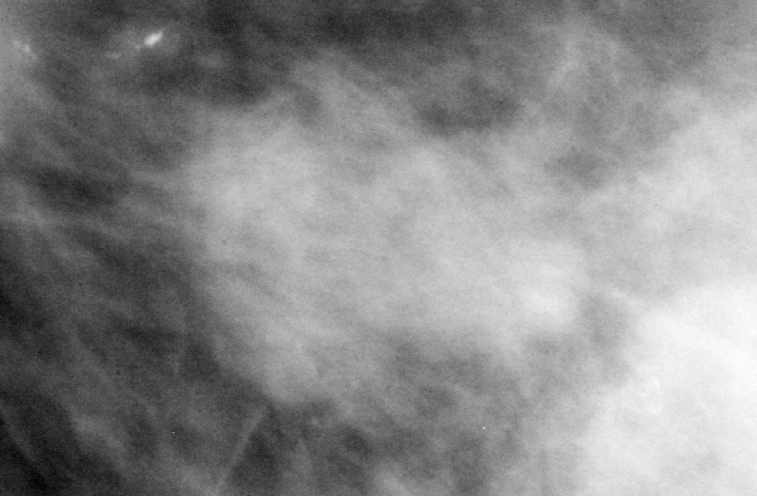
Region of interest cut from a scanned film mammogram (one marked finding), left breast, MLO view, BI-RADS breast density category 2 (scale 1–4).
- Marked abnormality: mass, shape irregular, margins spiculated; BI-RADS assessment category 5; subtlety rating 5 on a 1 (subtle) to 5 (obvious) scale; pathology result (as recorded, not read from the image): malignant.